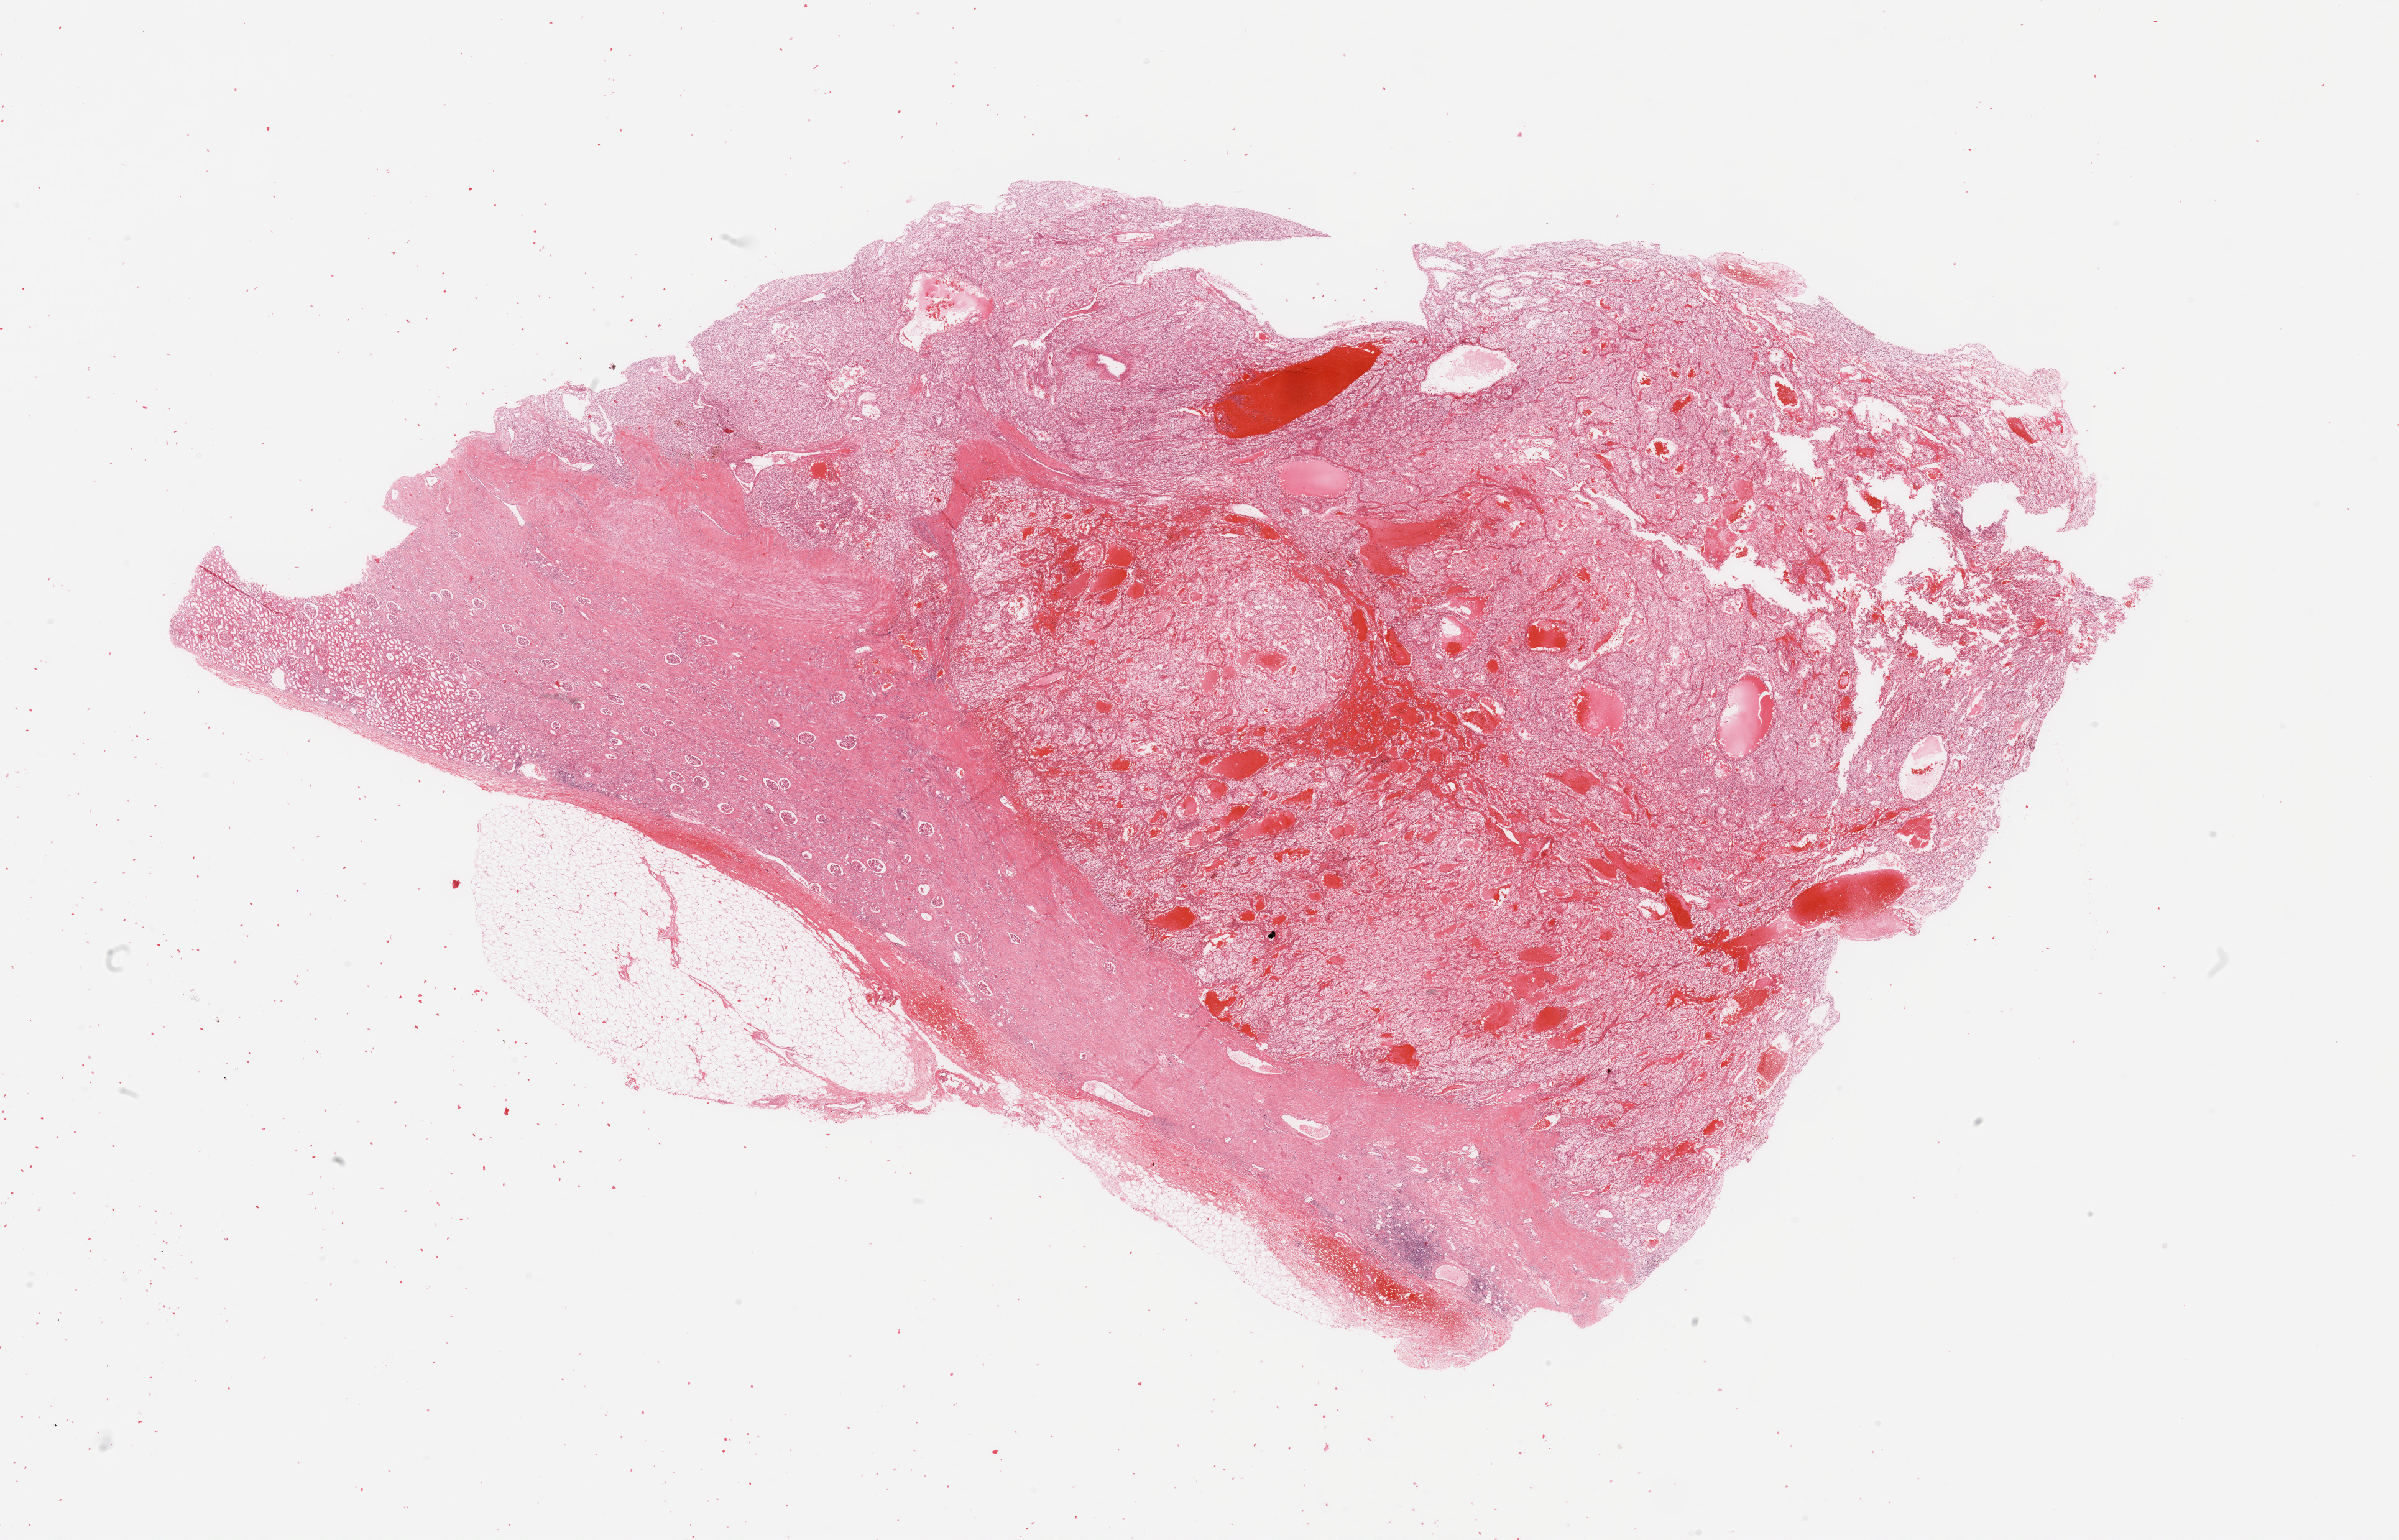
Digitized H&E-stained tissue section (whole slide) — whole scanned area (about 30.5 x 19.6 mm, slide scanned at 20x) shown as a low-resolution overview. Tumour tissue sample, sampled site: kidney. Male, 47 y/o. Histologic grade: G3 (poorly differentiated). Composition of this section per pathologist review: tumour nuclei 80%, necrosis 5%.
AJCC pathologic stage: I. Histologic diagnosis: Renal cell carcinoma, NOS.